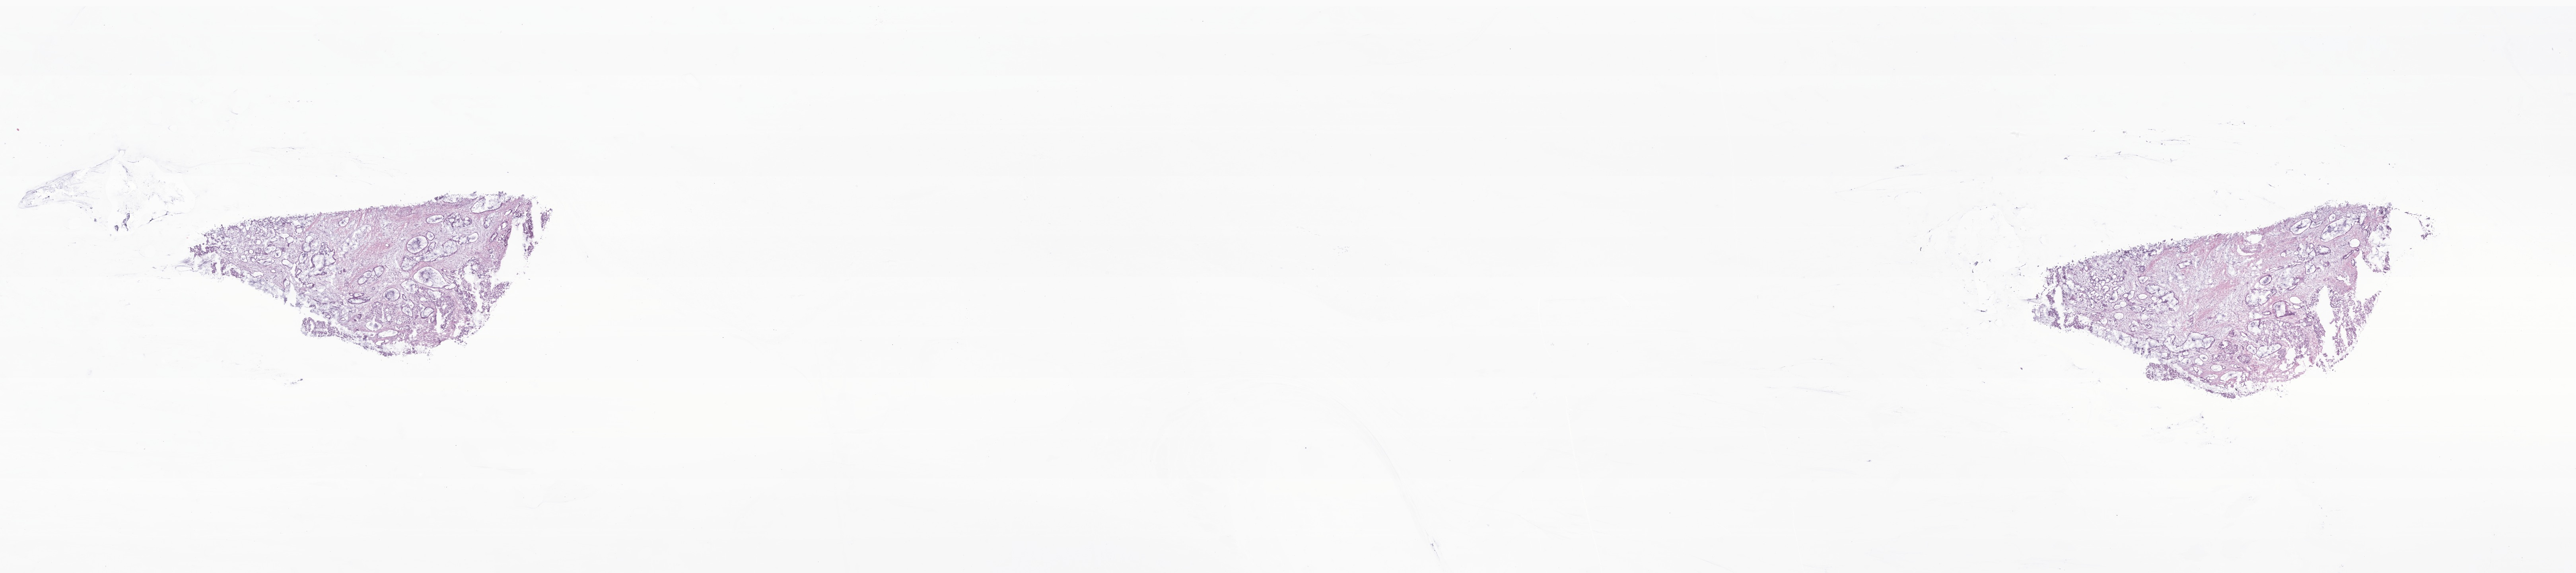
Haematoxylin and eosin whole-slide image of tumor tissue from the upper respiratory tract, shown as a low-resolution overview of the whole scanned area (about 27.3 x 6.1 mm); cryosection (OCT / tissue freezing medium). Male patient, age 50 months (4 years 2 months).
Recorded diagnosis: Carcinoma, NOS.